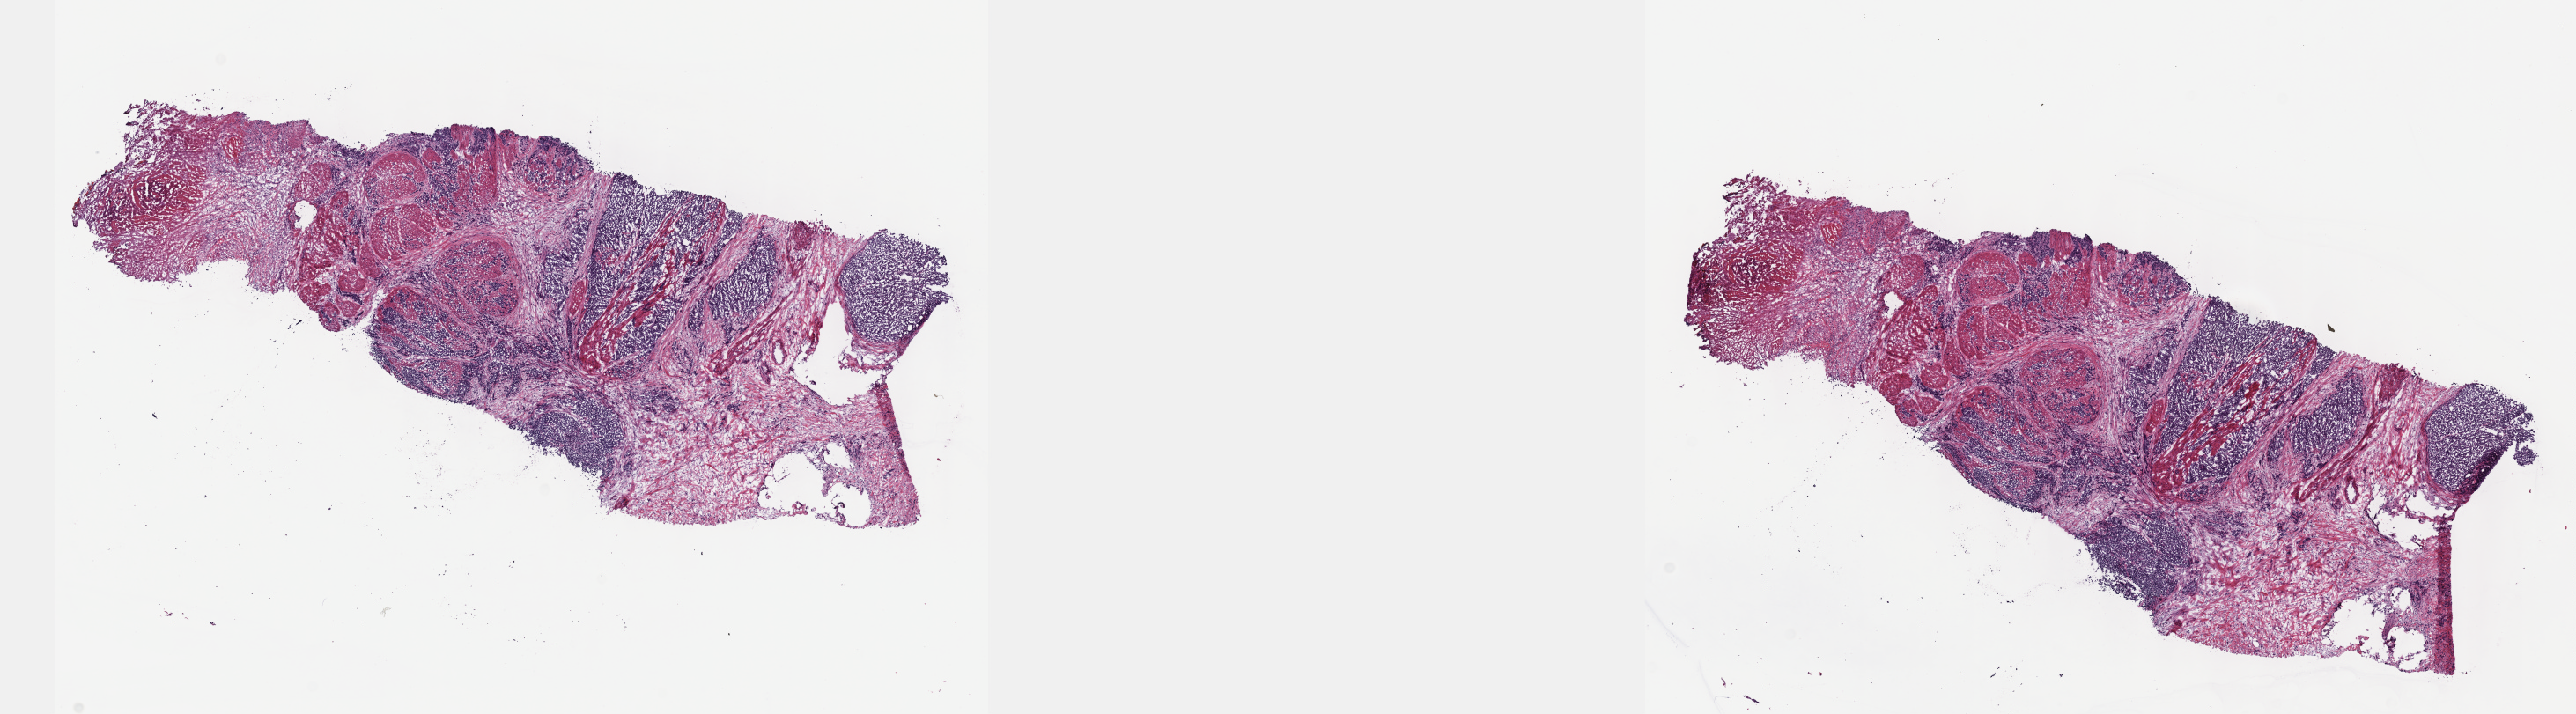
Digitized Hematoxylin and eosin (H&E) stained tissue section (whole slide), a low-resolution overview of the entire scanned area, about 23.6 x 6.6 mm; frozen section; sample: primary tumour, bladder. Male, age 68 years at initial diagnosis. Histologic grade: high grade. Slide review estimates, as recorded: tumour cells 60%, tumour nuclei 60%, normal cells 0%, stromal cells 40%, necrosis 0%. Inflammatory infiltration, as recorded: lymphocyte infiltration 5%, monocyte infiltration 0%, neutrophil infiltration 0%.
* pathologic diagnosis: Transitional cell carcinoma
* AJCC pathologic stage: IV
* TNM: T4 N2 MX
* lymph nodes positive (case pathology): 5 of 83 examined